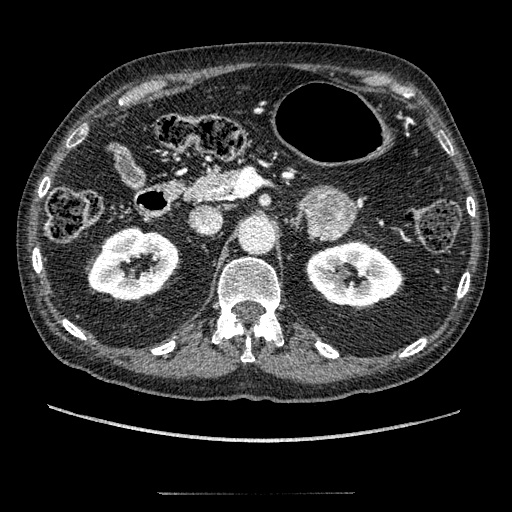
Contrast-enhanced abdominal CT, one axial slice; slice 121 of 274 in the series (ordered by position); intravenous contrast given; soft-tissue window (W 400 / L 40 HU); 1.25 mm slice thickness; 512 × 512 image matrix, field of view 381 × 381 mm. Patient: male, 69 years. From the clinical record (not read from this slice): diagnosis: adrenocortical carcinoma; tumour side: left adrenal; tumour size at pathology: 6.1 cm; Ki-67 index: 10 %; stage (as recorded): 3.
Structures marked on this image (semi-automatic segmentation, software-assisted and operator-edited):
- mass: box from (x=300, y=186) to (x=354, y=240) px